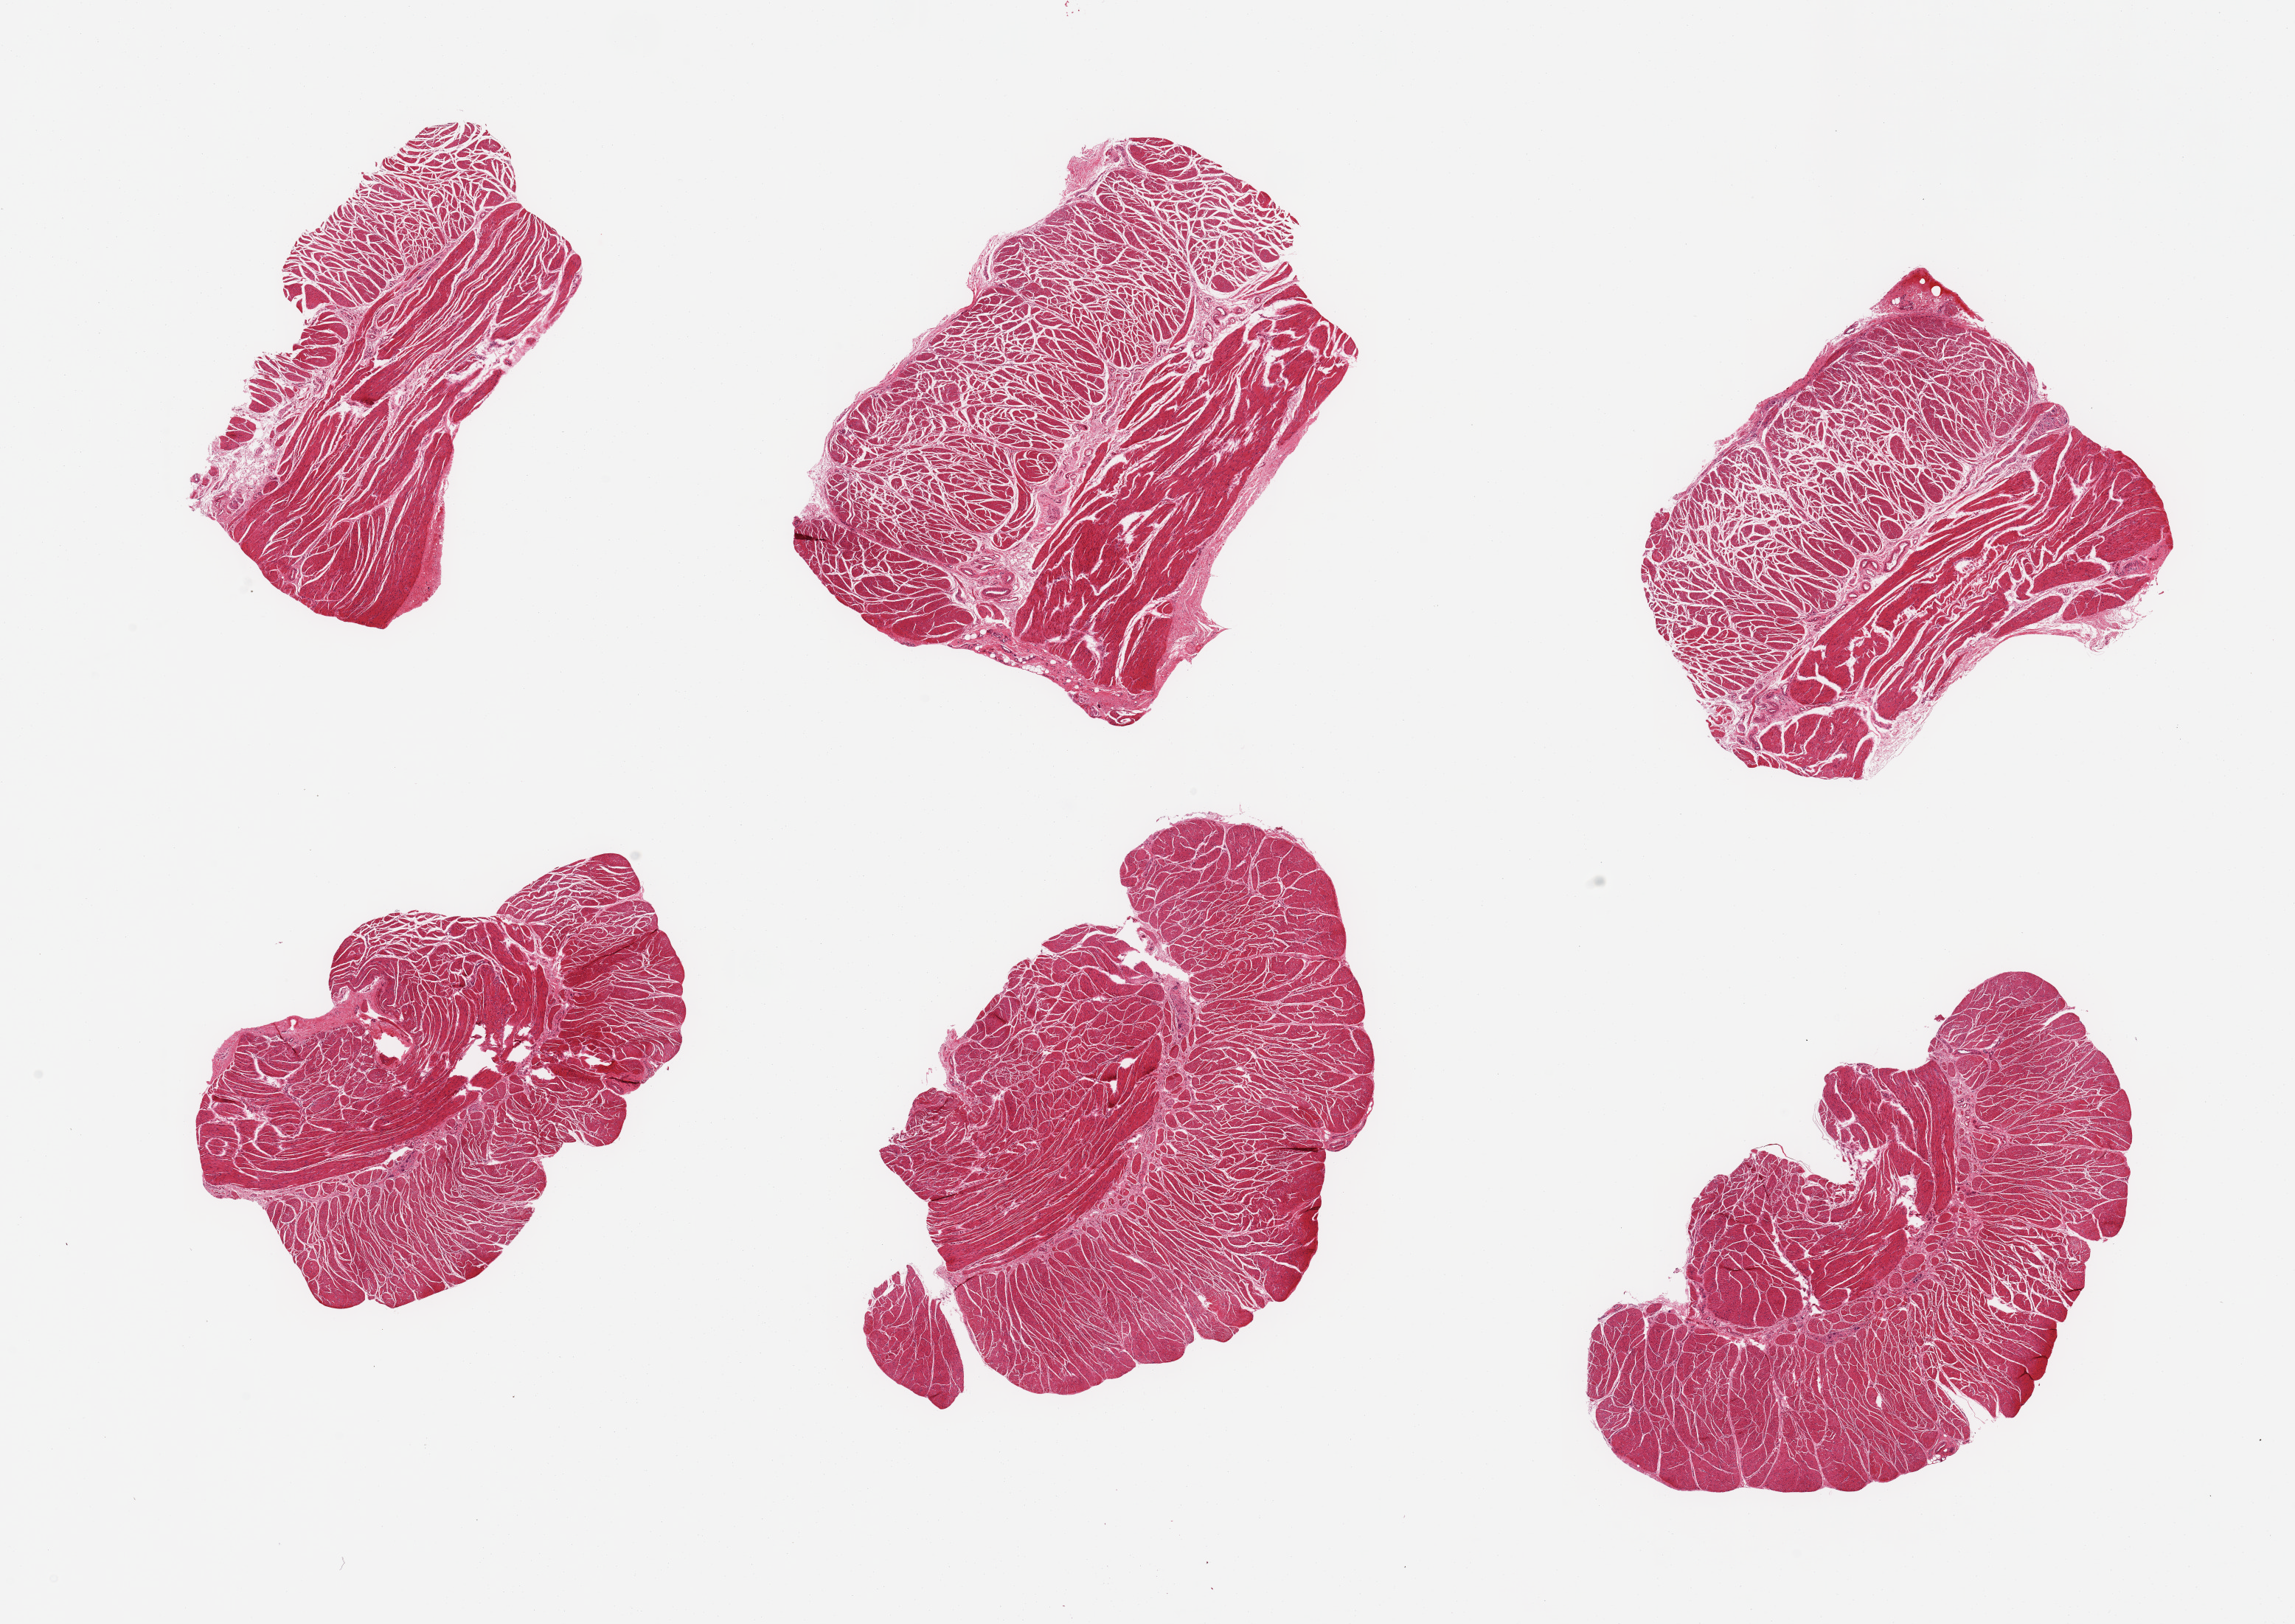
Hematoxylin and eosin (H&E) whole-slide image, brightfield — low-resolution overview of the scanned area, about 24.6 x 17.4 mm; PAXgene-fixed, paraffin-embedded tissue; sampled site (target tissue): esophageal muscle; tissue donor sample. Male donor.
Review note (as recorded): 6 pieces; well trimmed target muscularis.